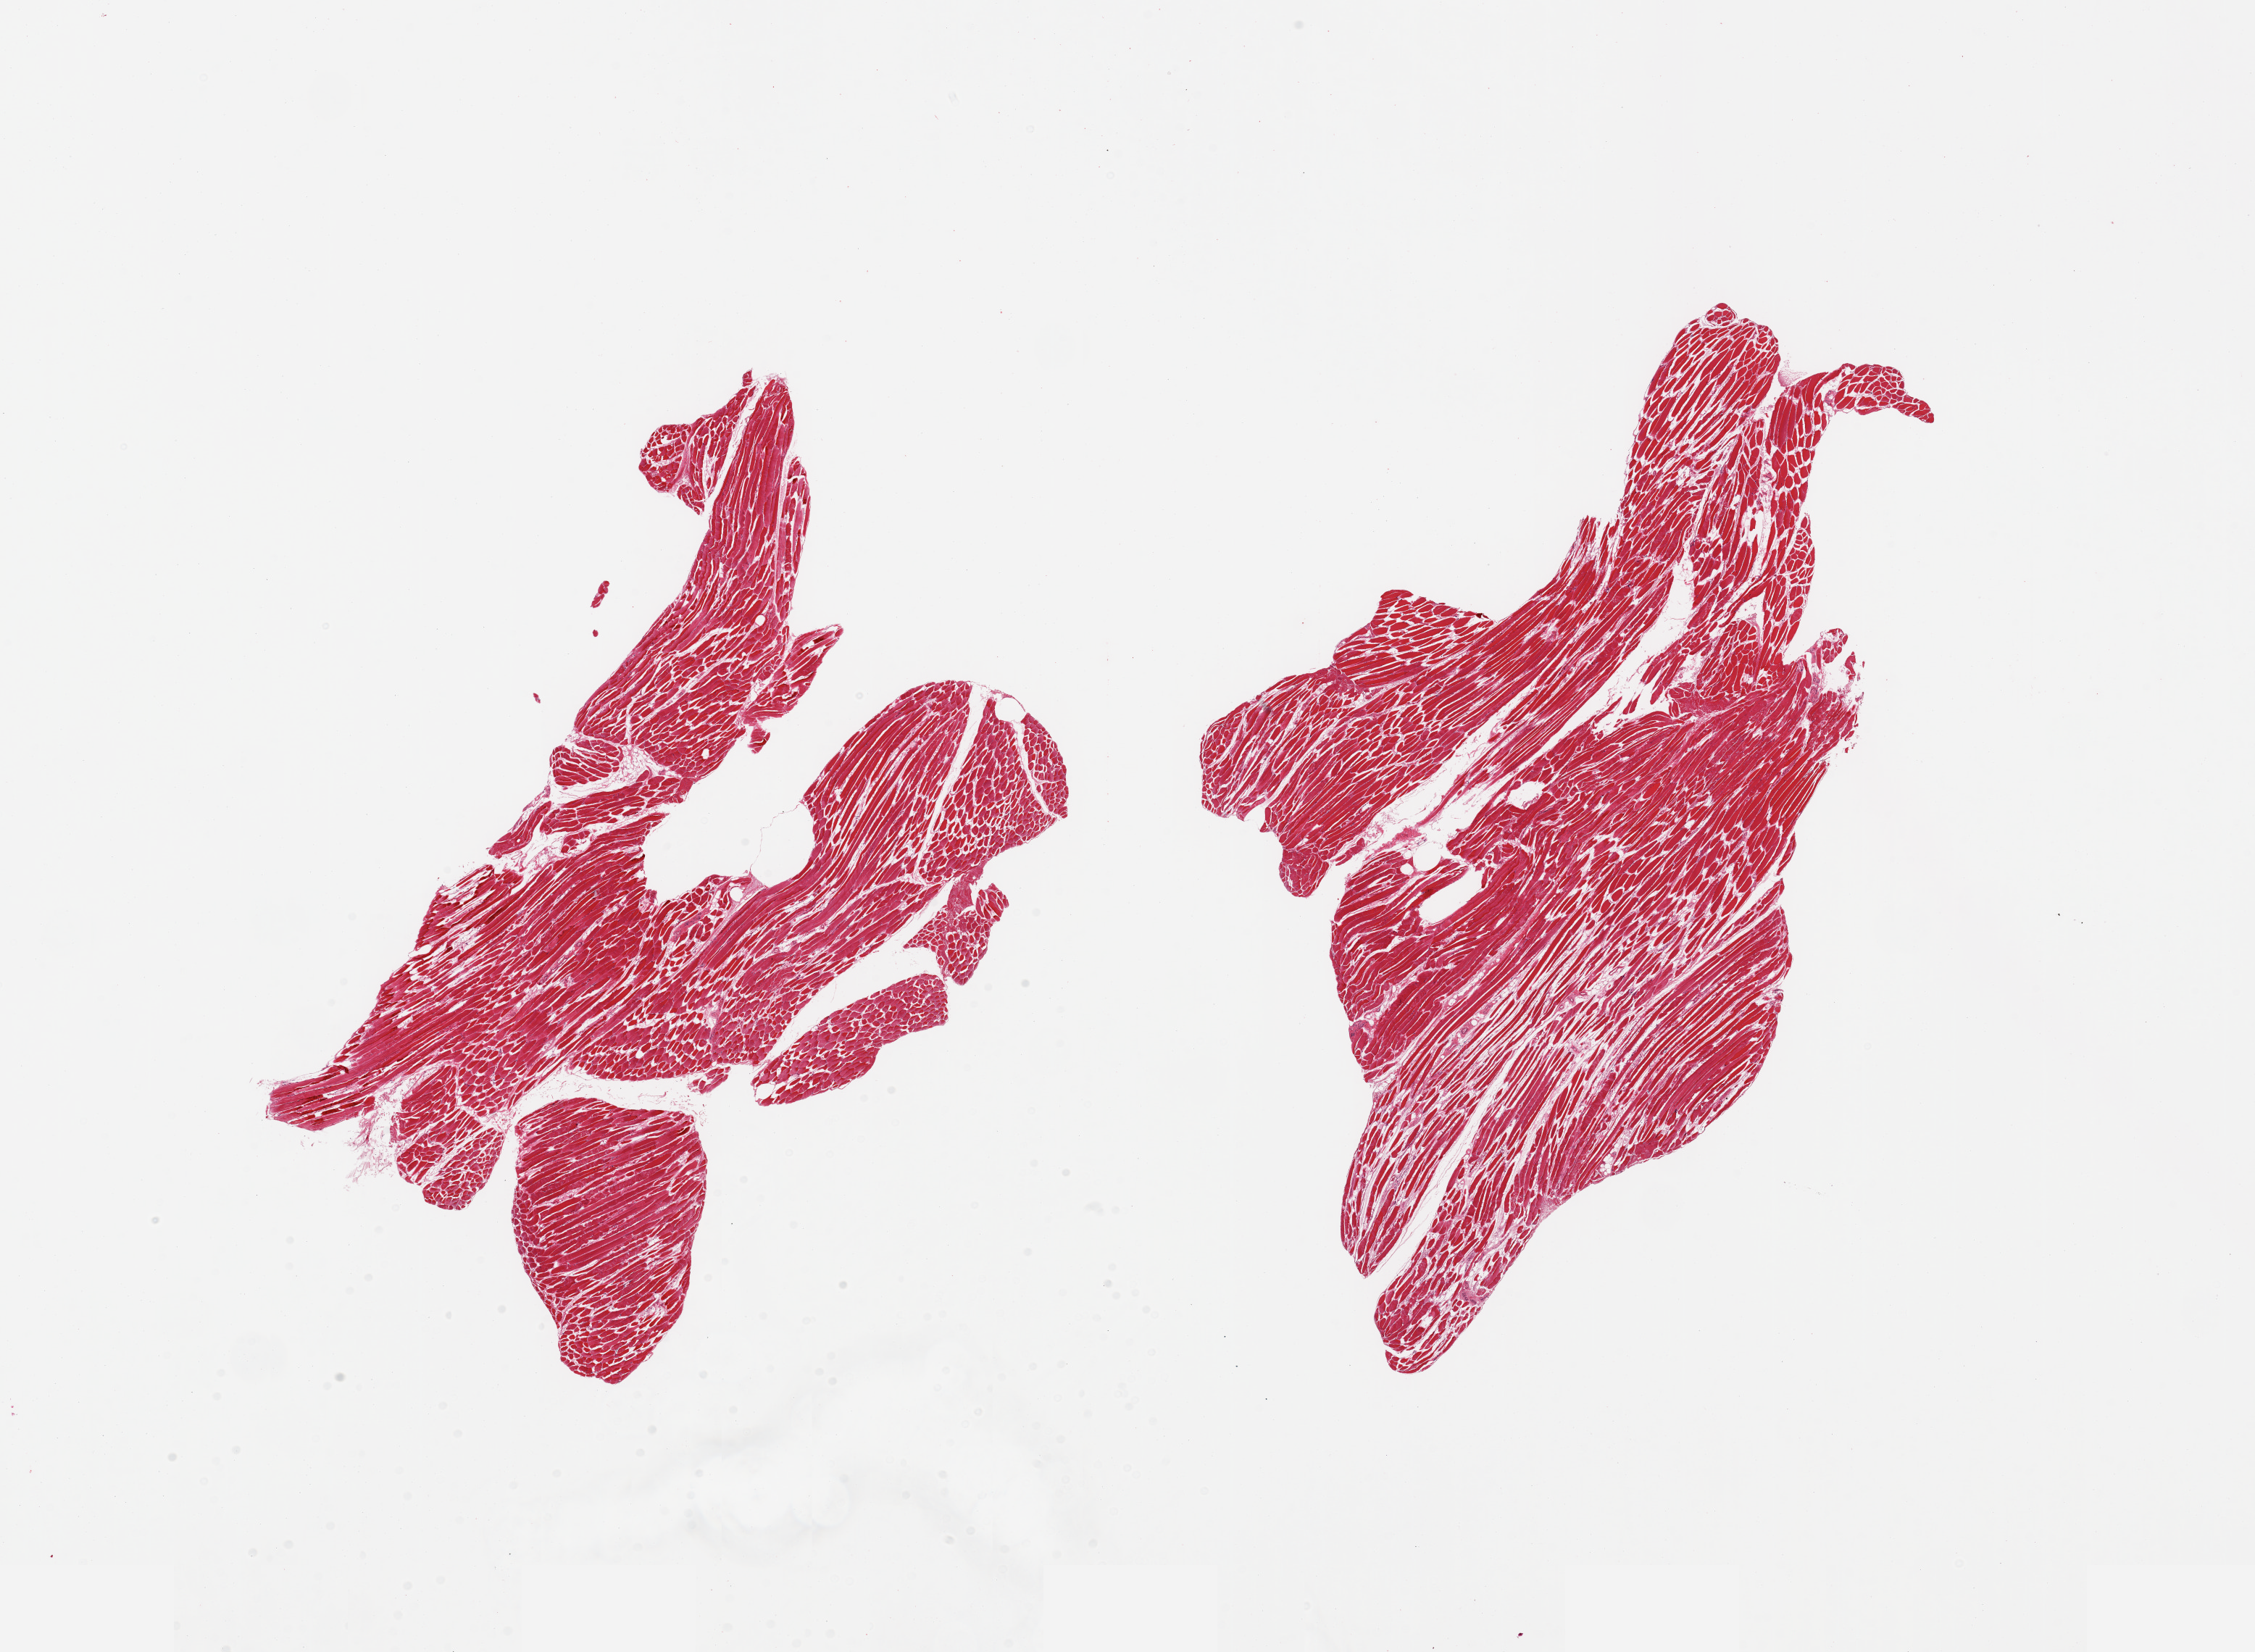
Digitized hematoxylin and eosin (H&E)-stained section — shown as a low-resolution overview of the whole scanned area (about 24.6 x 18.0 mm). PAXgene-fixed paraffin-embedded (PFPE) section. Section of skeletal muscle (target tissue). Donor tissue sample. Donor sex: male.
Review note (as recorded): 2 pieces; no fat content.